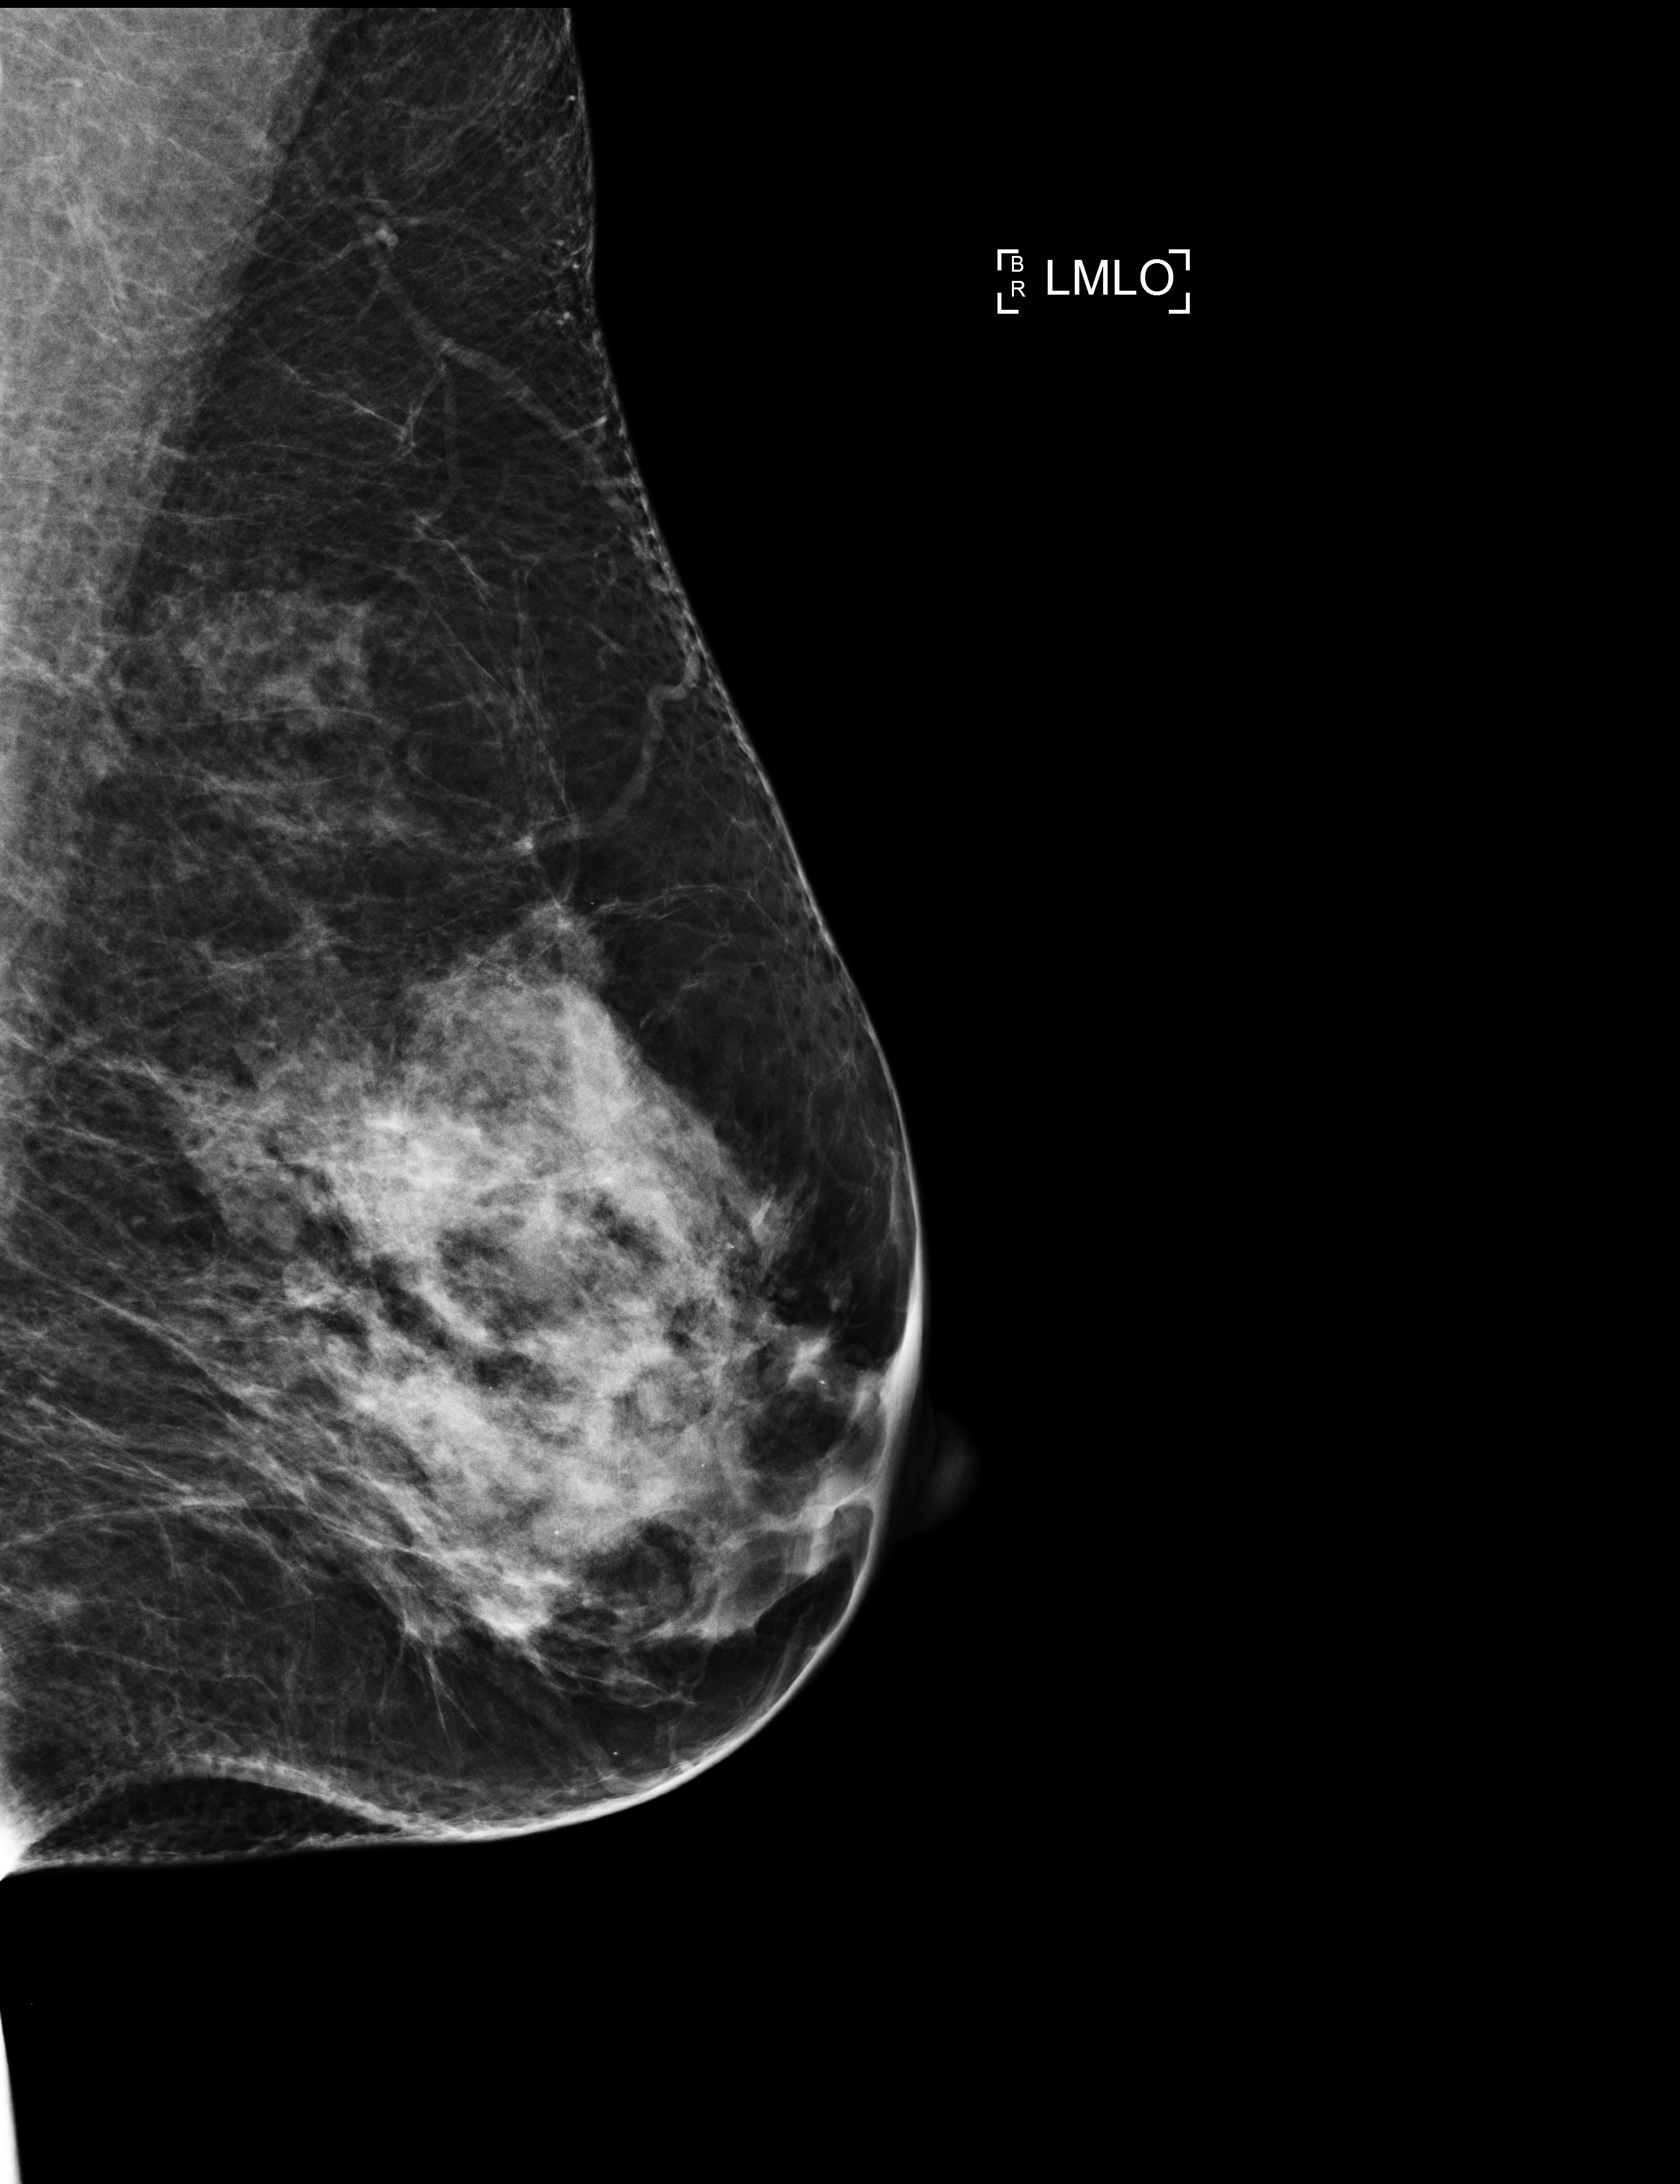
Annual screening mammography examination; compressed breast thickness 66 mm. Patient: female, 56 years.
Image type: full-field digital mammogram. Breast: left. Projection: MLO view.